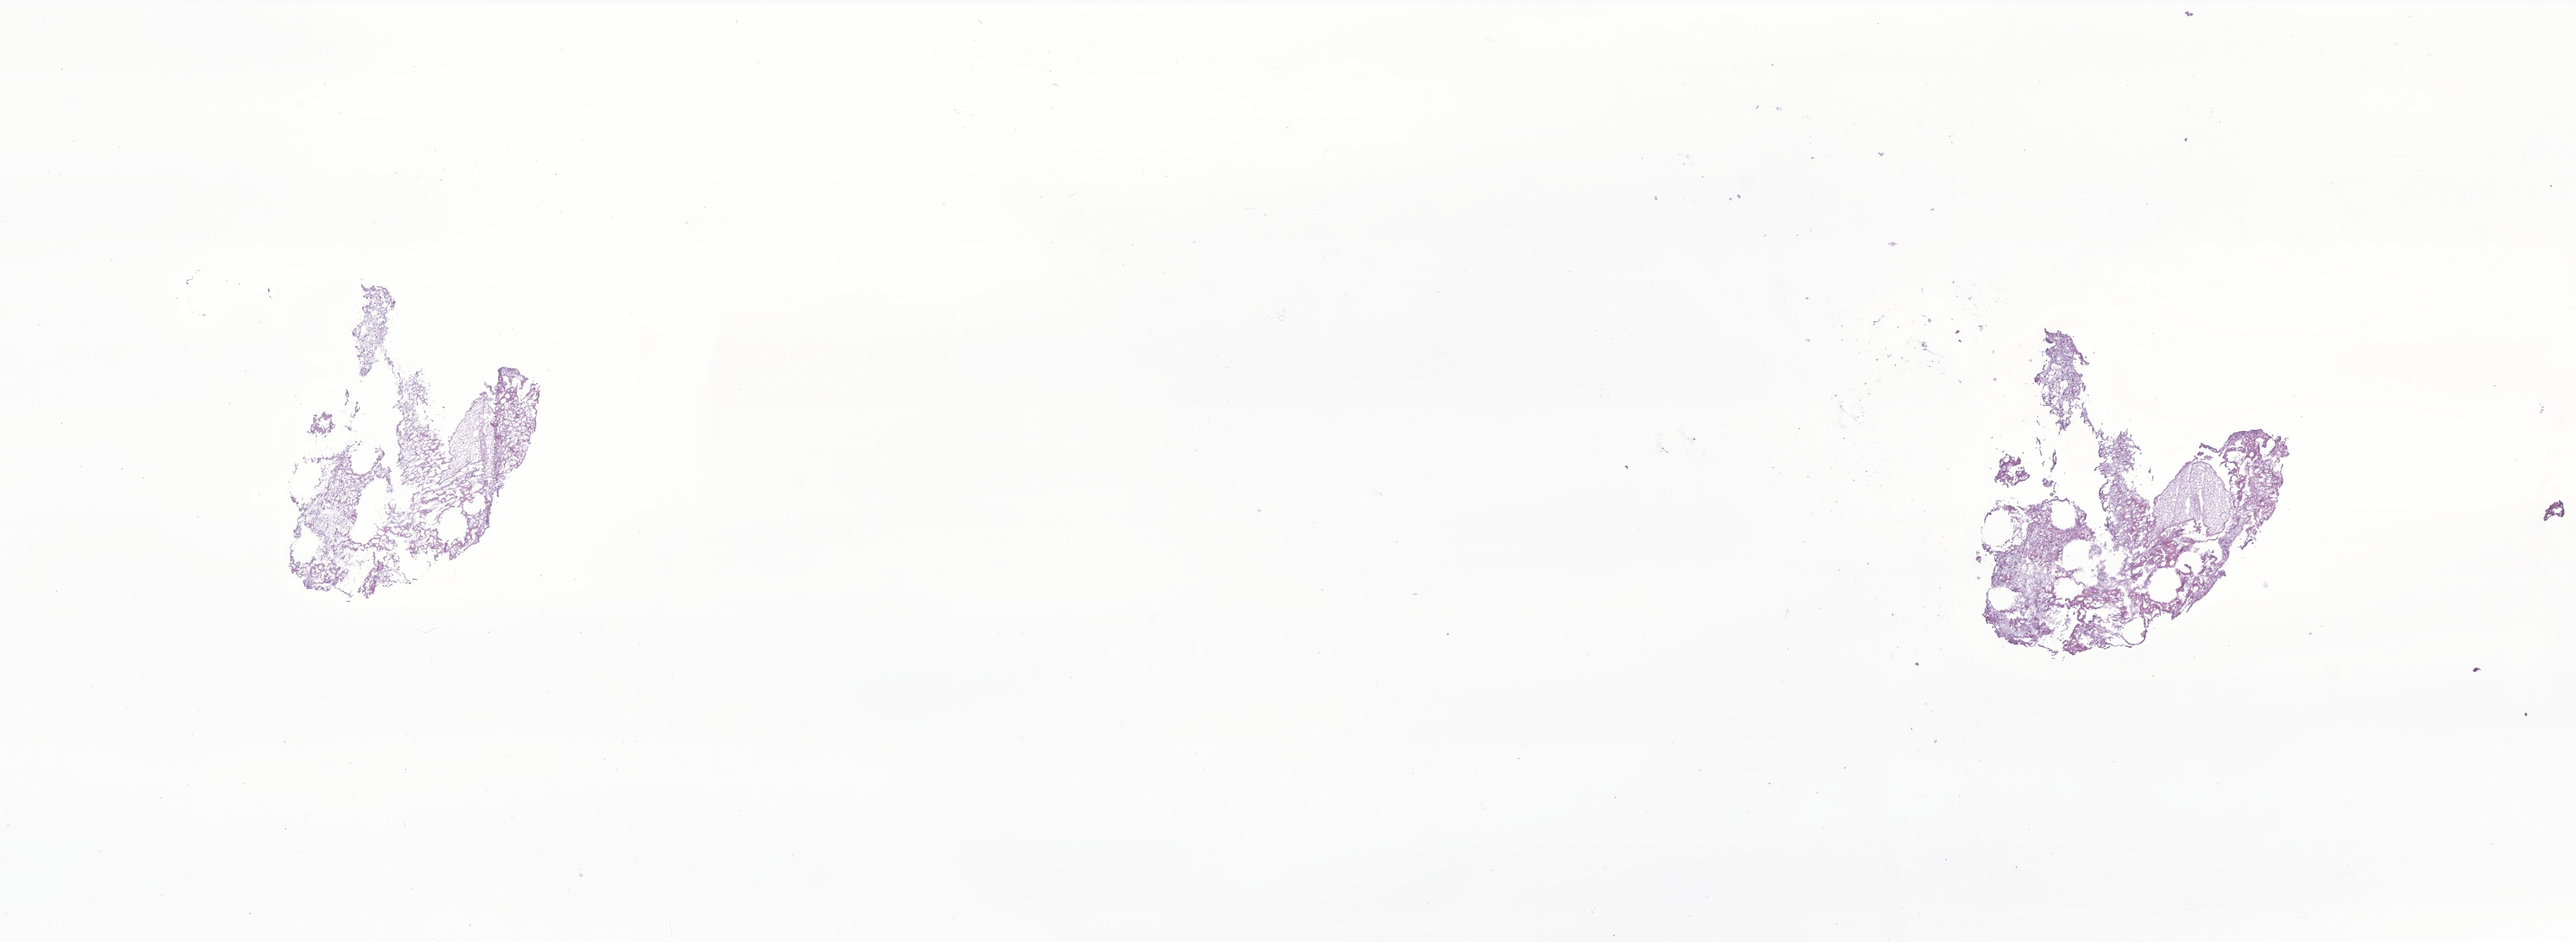
Digitized haematoxylin and eosin-stained section of tumor tissue from the spinal cord — a low-resolution overview of the entire scanned area, about 16.5 x 6.0 mm, frozen section (OCT-embedded). Female patient, age 64 months (5 years 4 months).
Diagnosis (ICD-O-3 morphology term): Pilocytic astrocytoma.